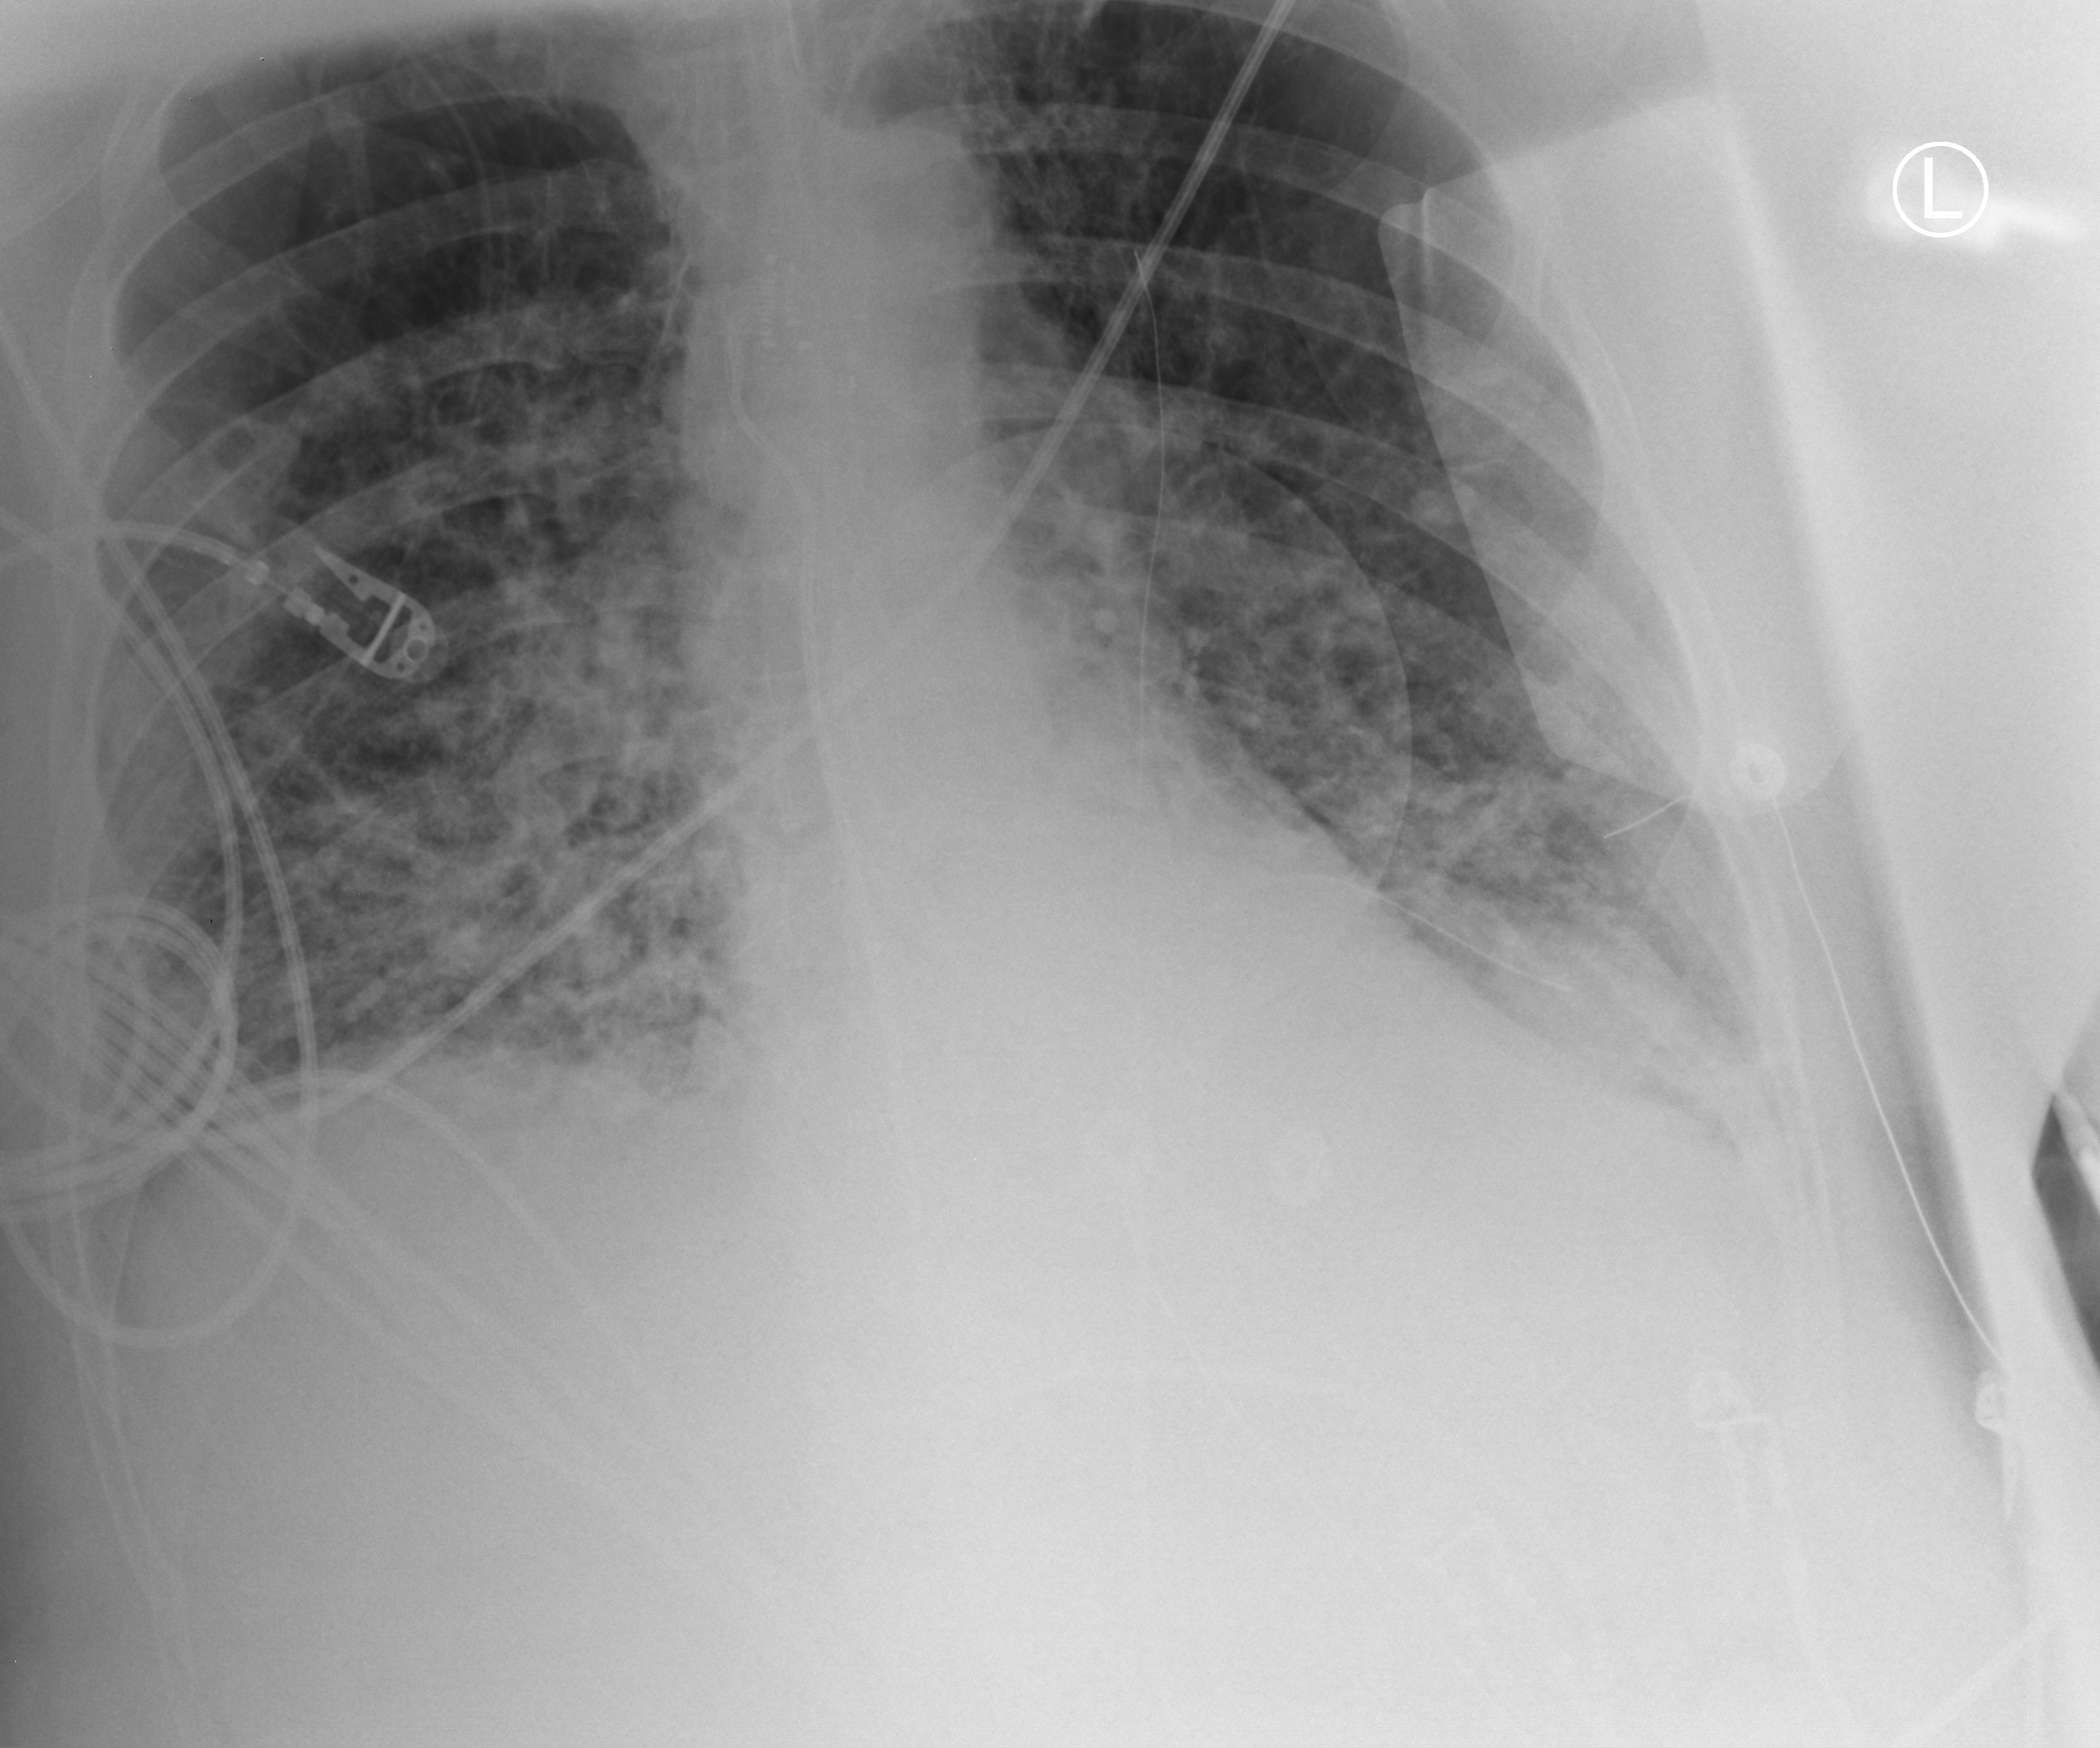
Bedside chest radiograph (computed radiography); anteroposterior (AP) projection. Adult patient hospitalised with COVID-19, age 18–59 years.
Admission-level facts for this patient (not findings on this image; timing relative to this image not recorded):
- mechanically ventilated during this hospital stay: yes
- other chronic lung disease (admission record): yes
- chronic kidney disease (admission record): no